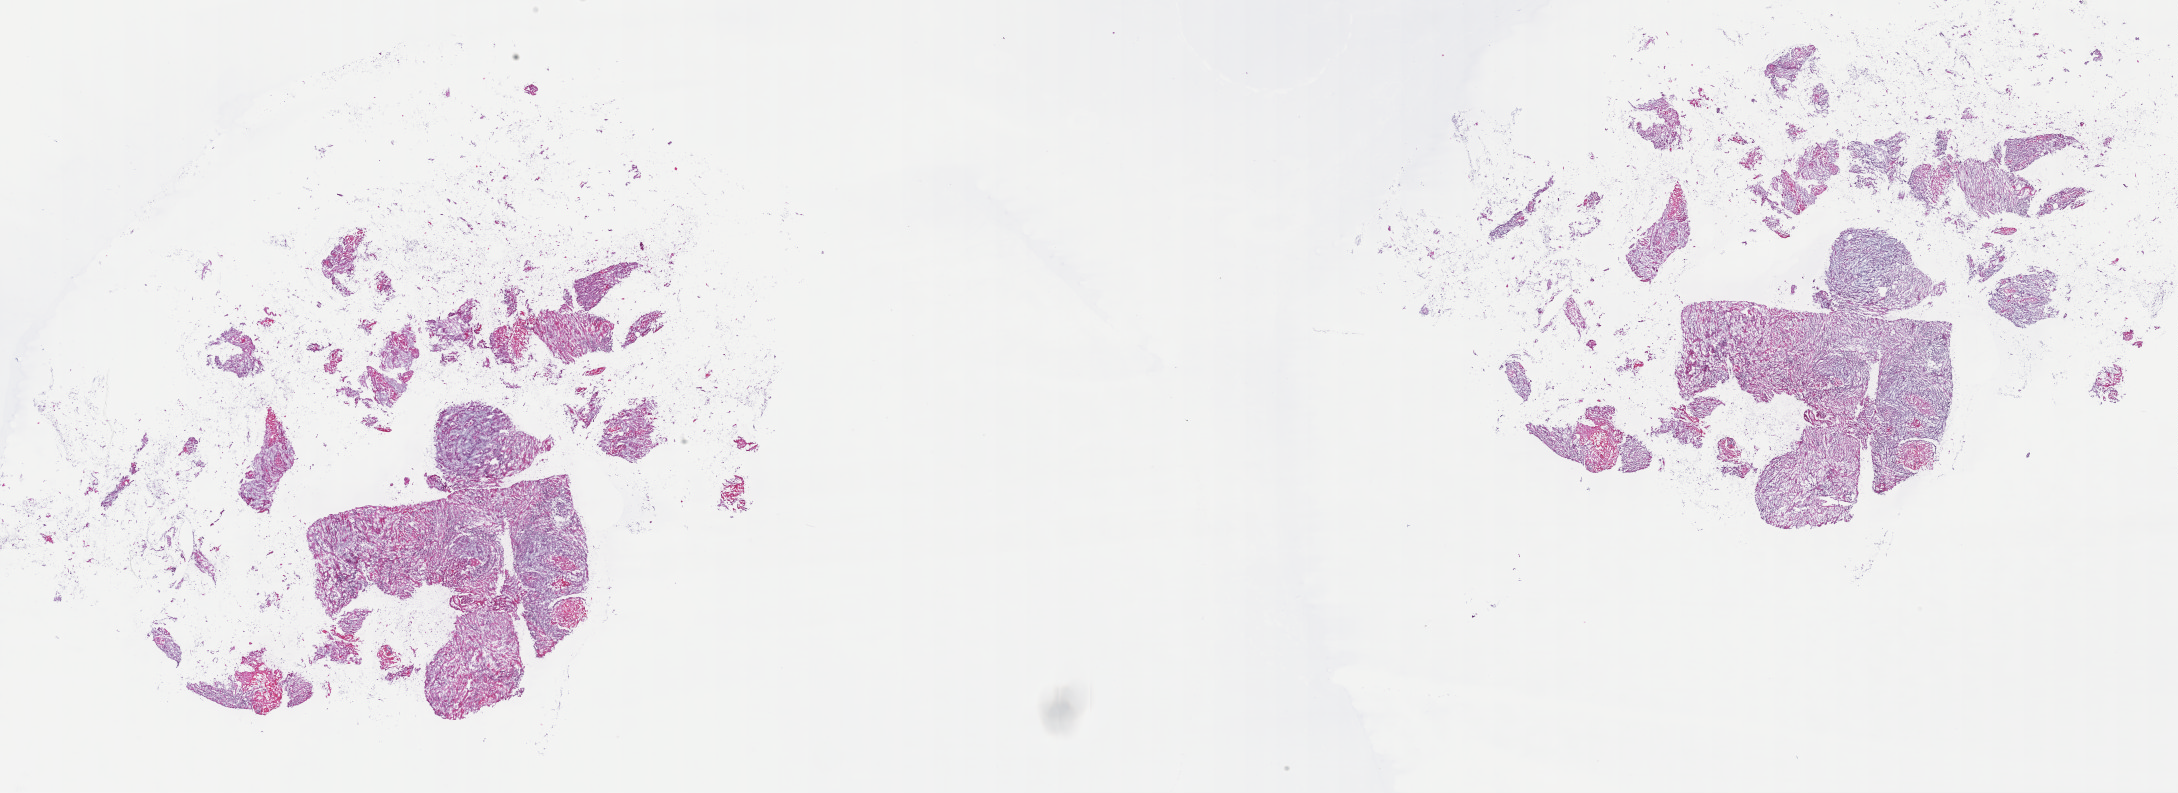
H&E-stained whole-slide image, whole scanned area (about 35.2 x 12.8 mm) shown as a low-resolution overview; FFPE section; primary tumour sample from the head and neck. Male, age 41 years at initial diagnosis. Histologic grade: G2 (moderately differentiated).
AJCC pathologic stage: IVA (7th edition). Diagnosis: Squamous cell carcinoma, NOS (tongue, NOS).